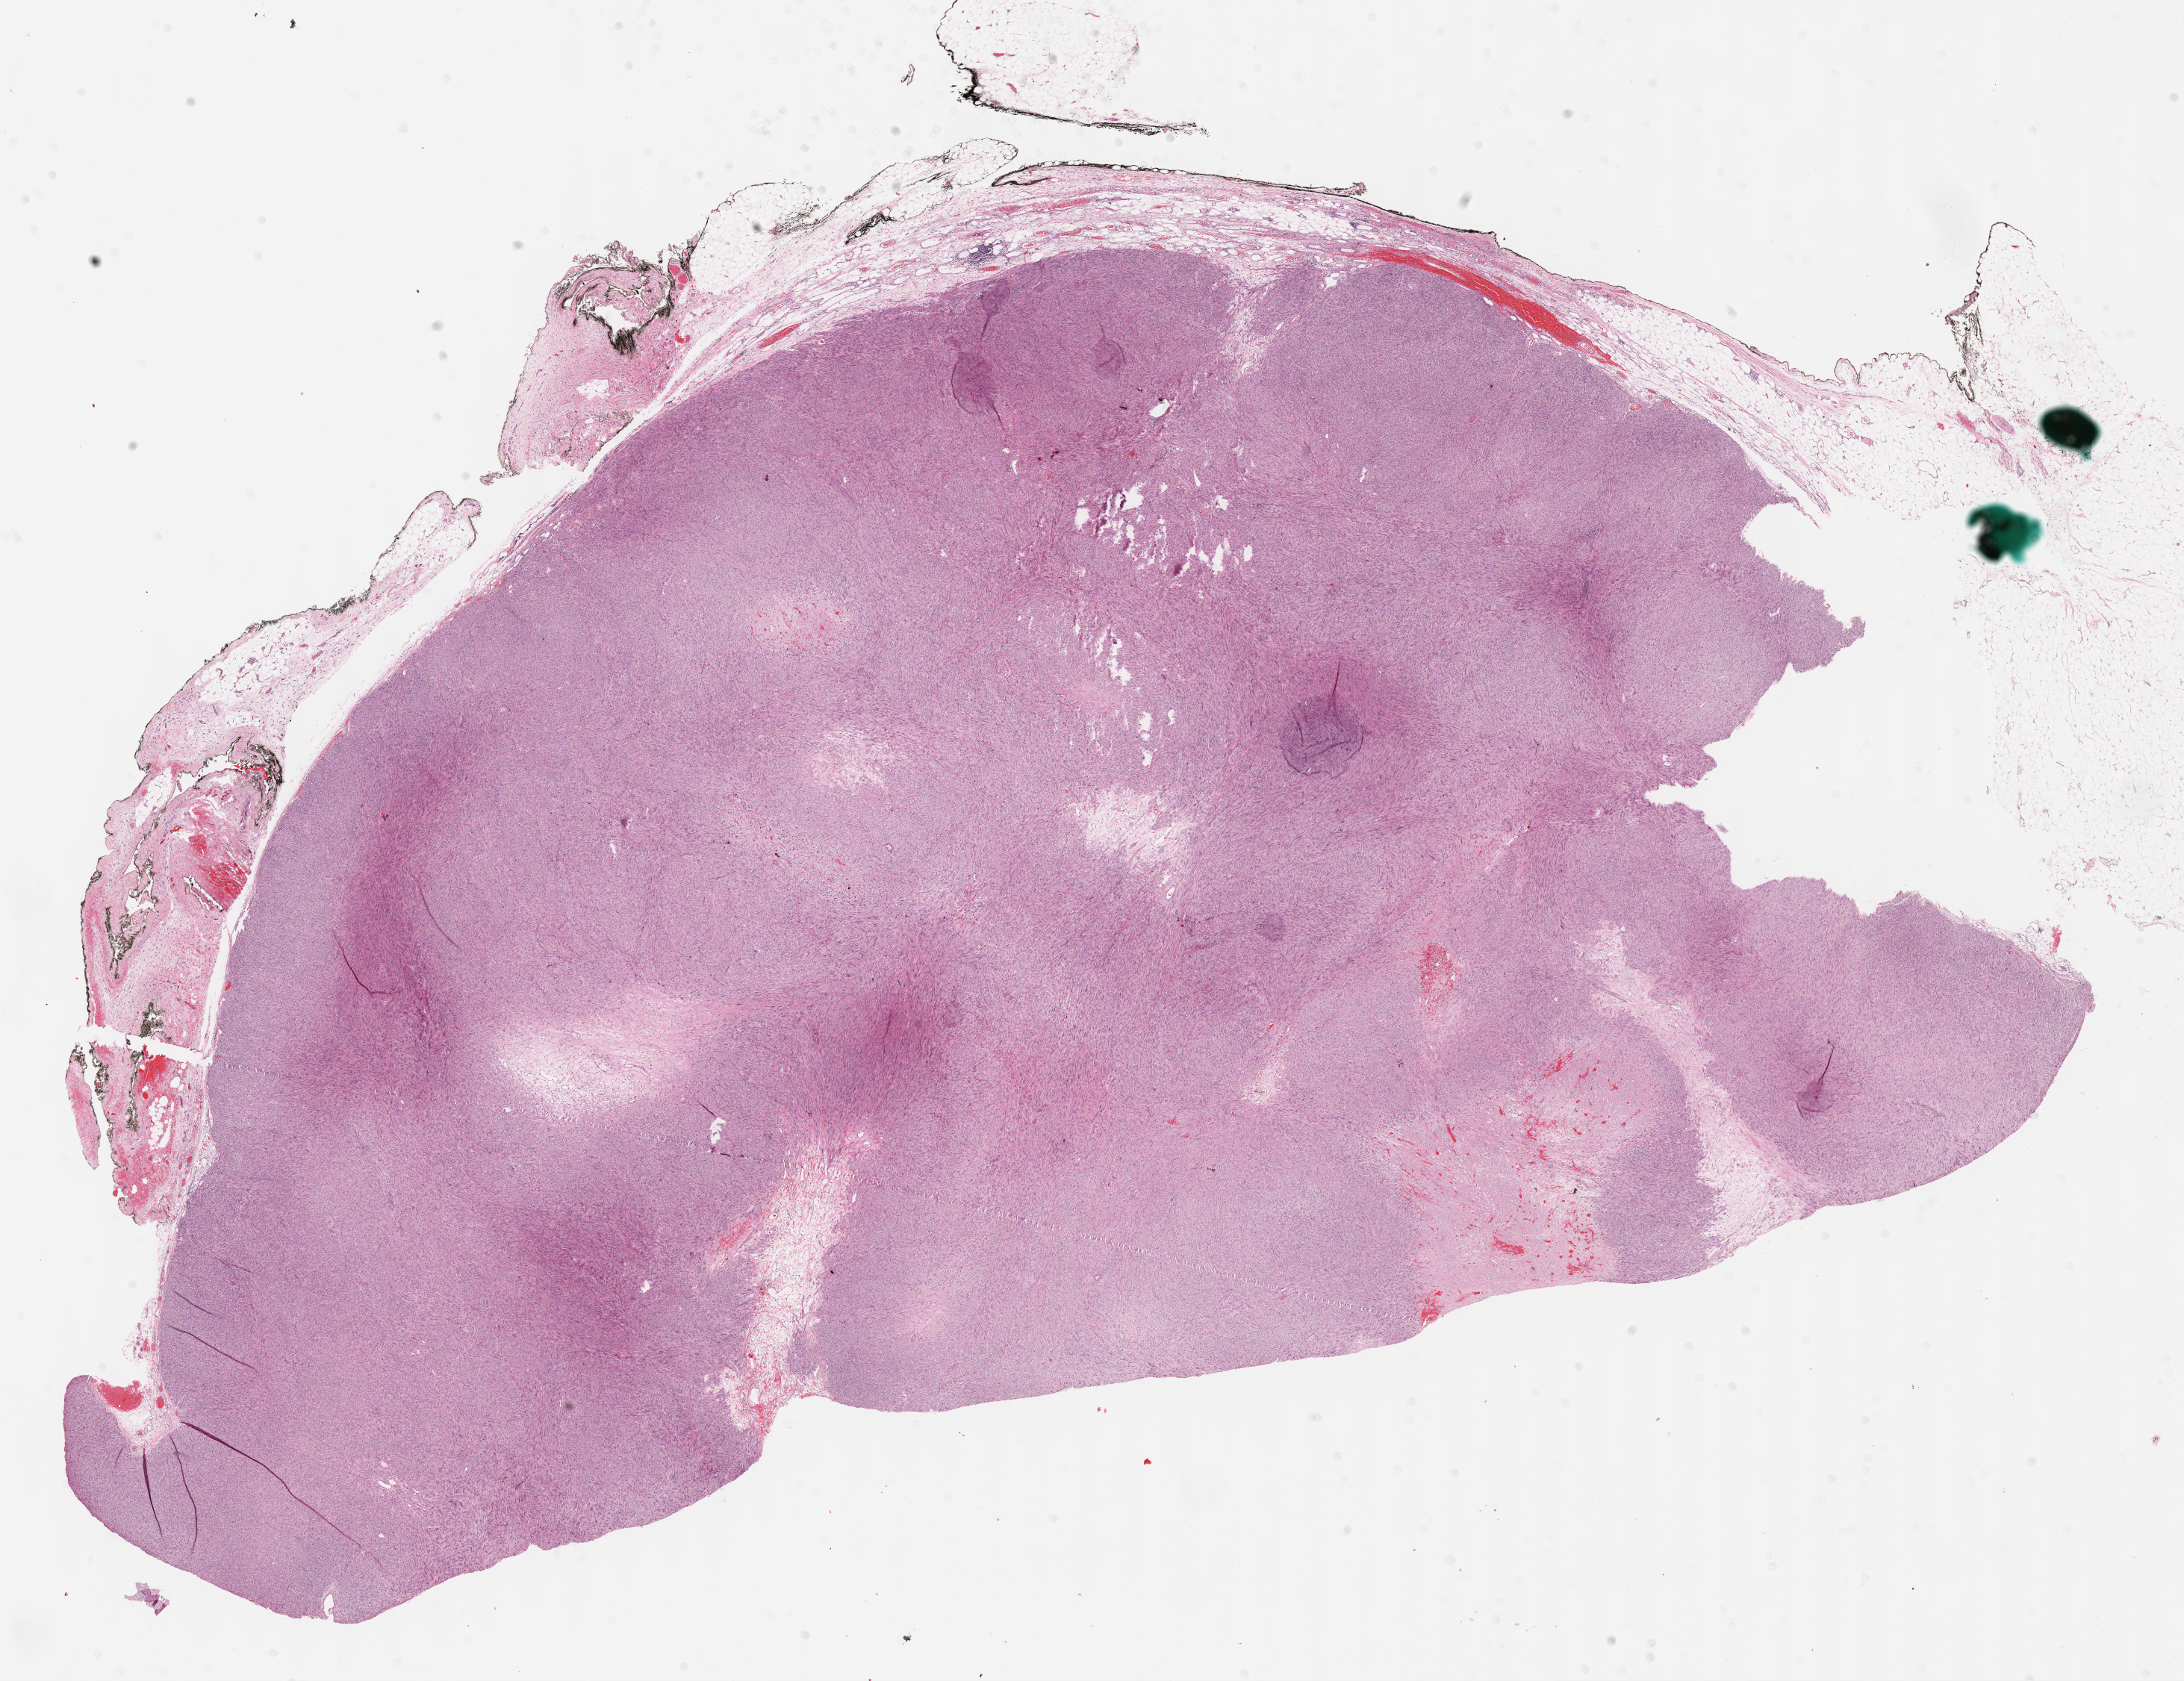
Whole-slide histology image, H&E-stained — whole scanned area (about 23.7 x 18.2 mm) shown as a low-resolution overview, formalin-fixed paraffin-embedded (FFPE) diagnostic section, retroperitoneum and peritoneum, primary tumour sample. Male, age 61 years at initial diagnosis.
Histologic diagnosis: Leiomyosarcoma, NOS (retroperitoneum).